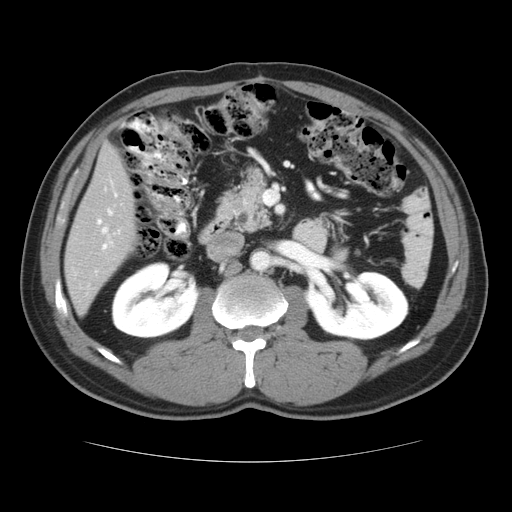
Contrast-enhanced abdominal CT, one axial slice; slice 15 of 37 in the series (ordered by position); soft-tissue window (W 400 / L 40 HU); 512 × 512 image matrix, field of view 374 × 374 mm. Male patient, age 66 years. Case-level facts recorded for this patient, not image findings: diagnosis: colorectal cancer liver metastases, imaged before liver resection; multiple liver metastases: yes; largest metastasis: 1.6 cm; disease in both lobes: yes.
Annotated regions visible in this slice (outlined manually by an expert reader):
- hepatic veins: bounding box (x1, y1, x2, y2) in pixels: (101, 189, 113, 246)
- liver: (65, 142, 138, 315)
- planned liver remnant (the part of the liver to remain after resection): (66, 189, 138, 314)
- portal vein (with intrahepatic branches): (97, 194, 117, 249)